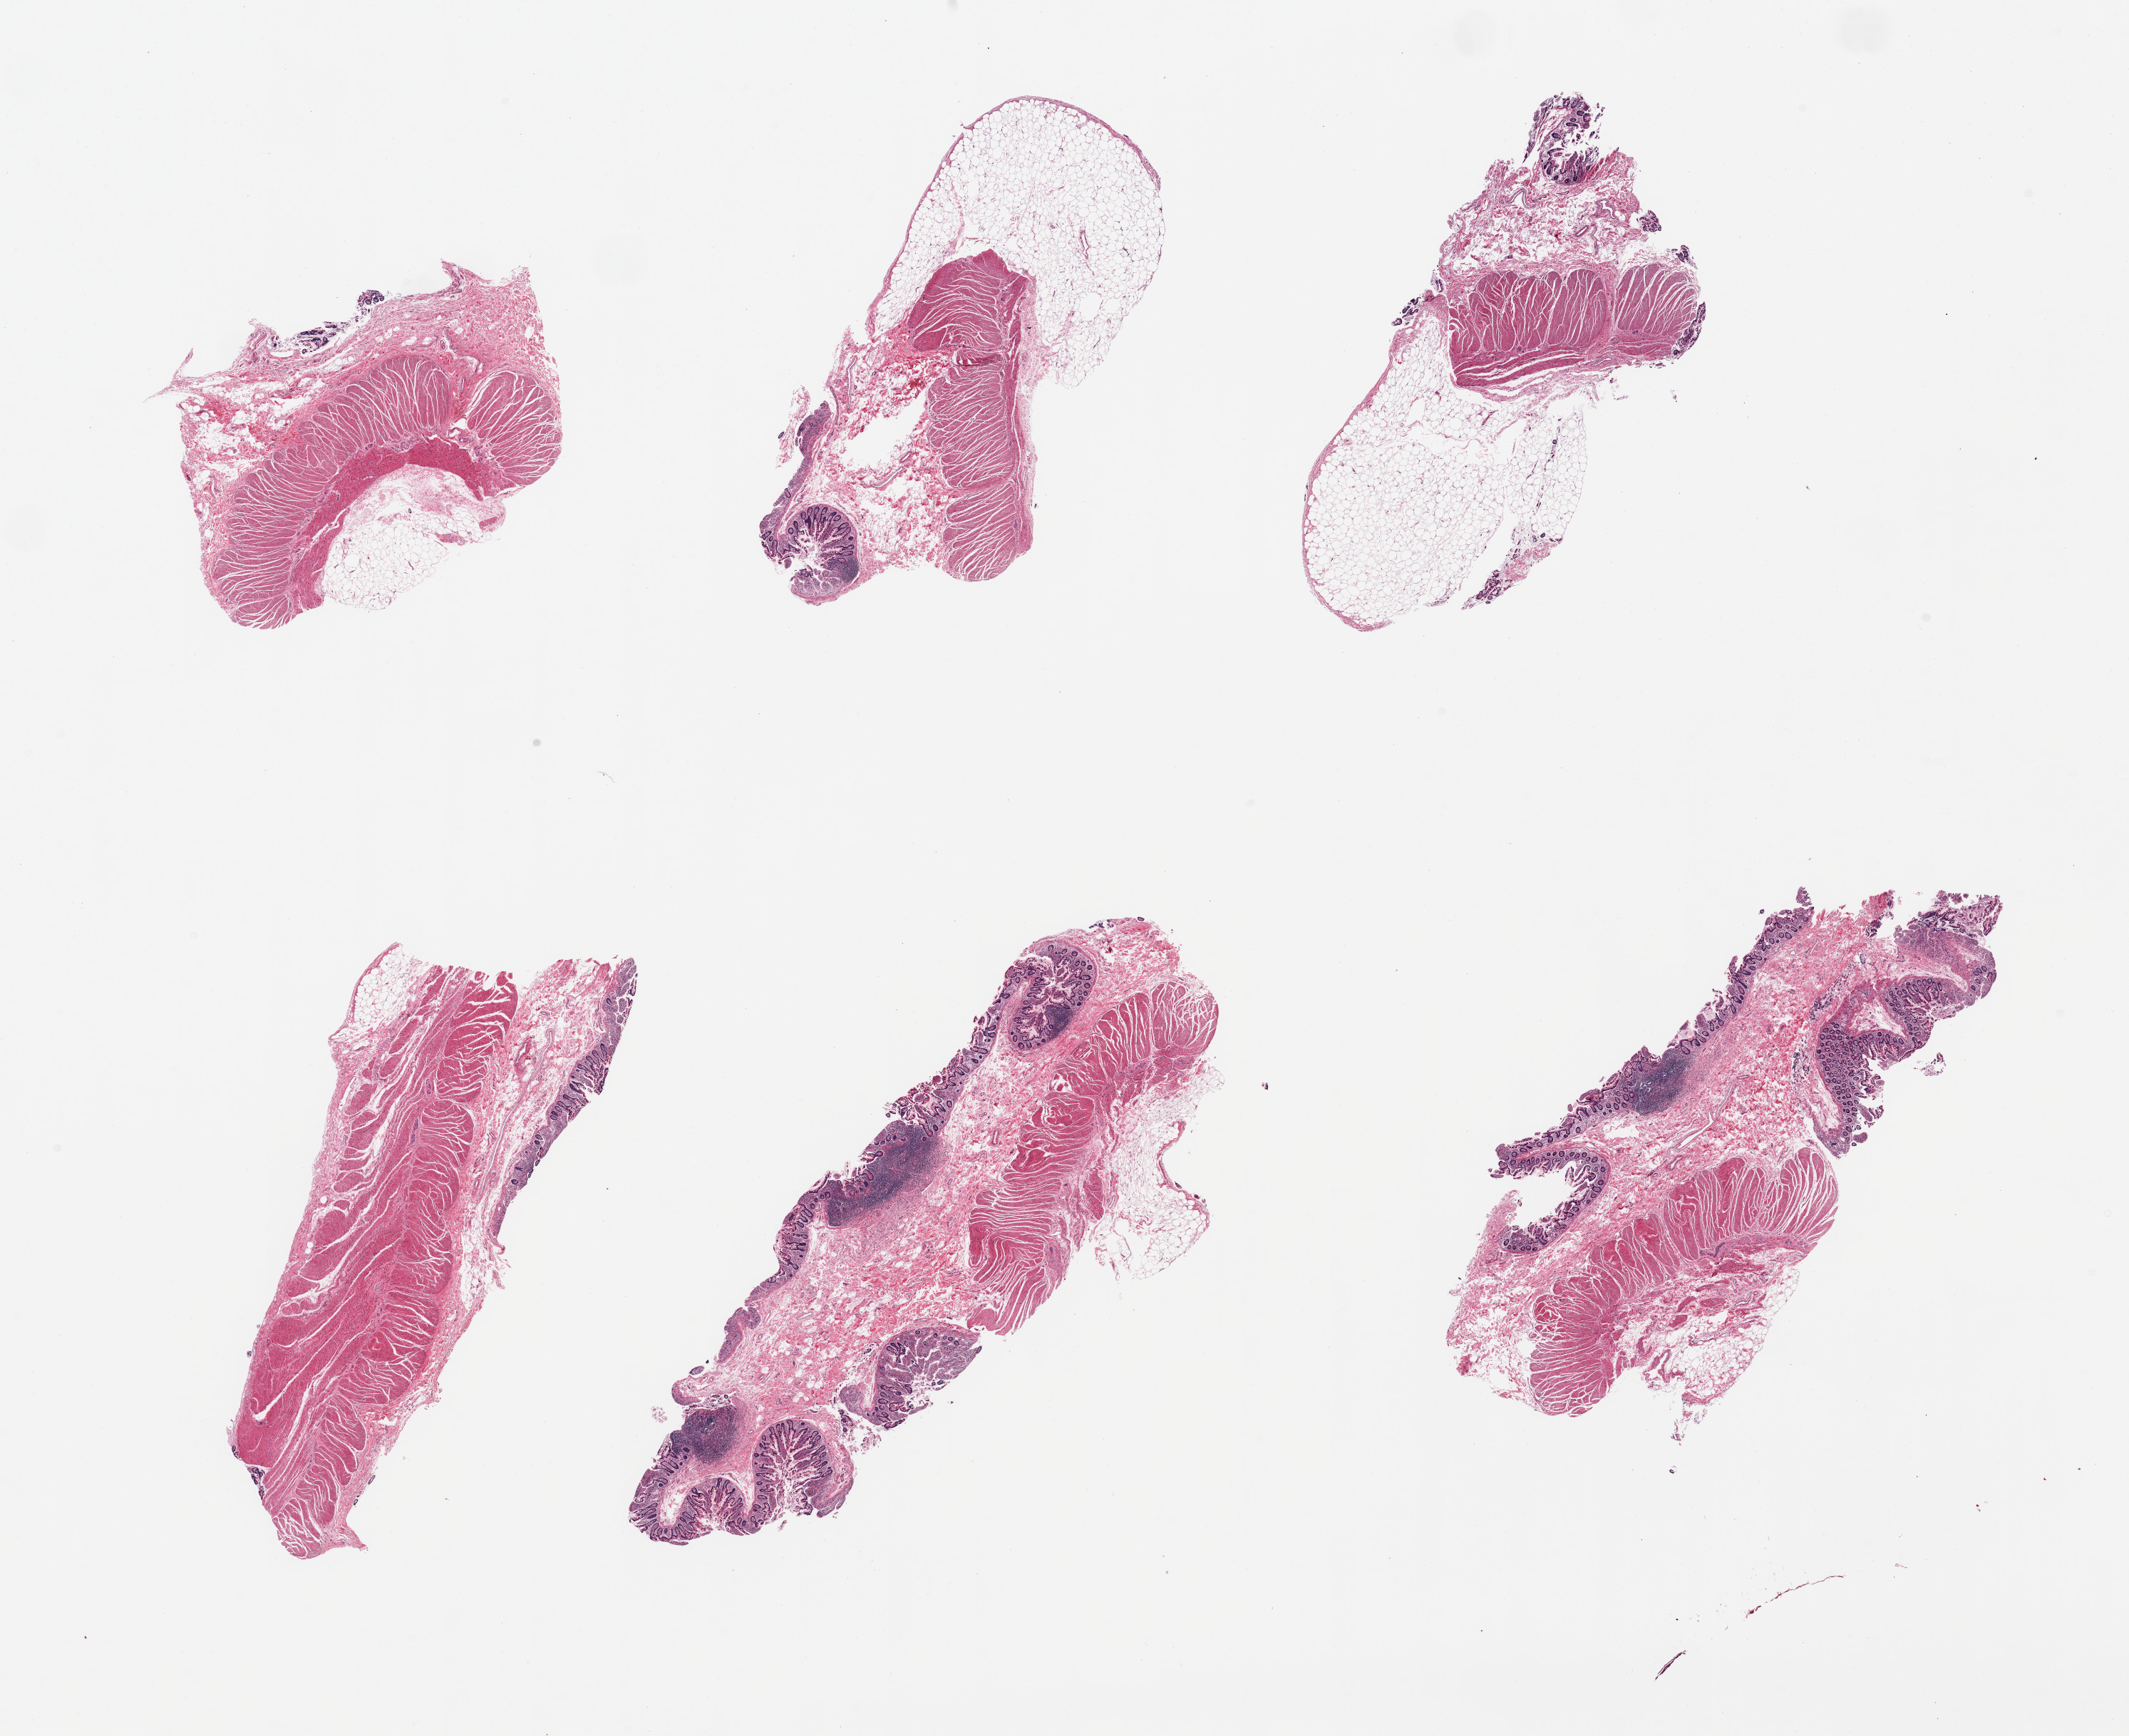
Haematoxylin and eosin whole-slide image, brightfield, a low-resolution overview of the entire scanned area, about 23.6 x 19.3 mm.
Specimen: PAXgene-fixed, paraffin-embedded tissue; target tissue: ileum; donor tissue sample.